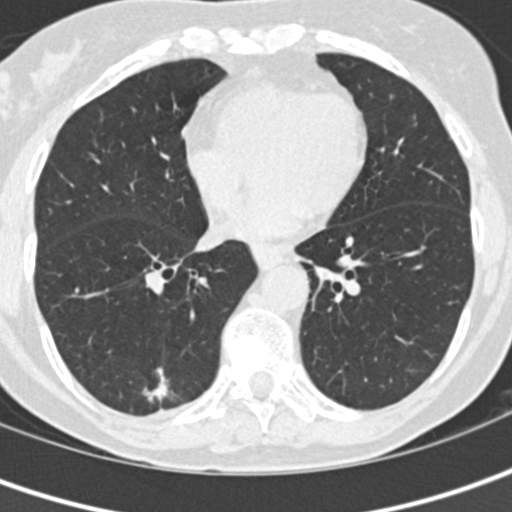
Low-dose screening chest CT, one axial slice; position 62 of 152 along the scan axis; 120 kVp; lung window (W 1500 / L -600 HU); 2 mm slice thickness; 512 × 512 image matrix, field of view 280 × 280 mm.
Annotated regions visible in this slice (manually delineated by an expert):
- lesion 1 (tumor, lower lobe of right lung): box from (x=142, y=367) to (x=169, y=402) px